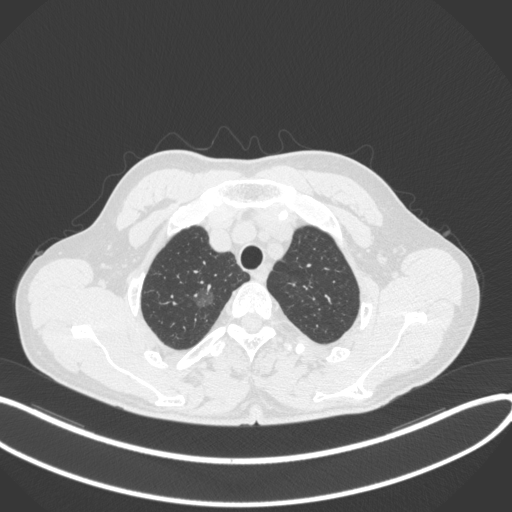
Chest CT, one axial slice. Position 323 of 407 along the scan axis. Reconstruction kernel B31f. 120 kVp. Lung window (W 1500 / L -600 HU). 1 mm slice thickness. 512 × 512 image matrix. Patient: male, 58 years. From the clinical record (not read from this slice): clinical TNM (as recorded): T1c N0 M0.
Outlined on this slice (rectangle marked by the reading radiologist):
- lung tumour (recorded histology: adenocarcinoma): bounding box [x1, y1, x2, y2] px = [187, 276, 228, 315]